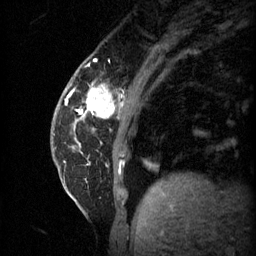
Breast MRI (dynamic contrast-enhanced), one sagittal slice. Position 13 of 60 along the scan axis. 3 images stored at this slice position (order not interpretable as contrast timing). 1.5 T. TE 4.2 ms, TR 11 ms. 2 mm slice thickness. 256 × 256 image matrix. Female patient, age 62 years.
Structures marked on this image (semi-automatically segmented with operator editing):
- analysis volume of interest (the breast-tissue region the enhancement analysis was run in; not a lesion): bounding box (x1, y1, x2, y2) in pixels: (55, 72, 124, 131)
- tumour enhancement mask (voxels above the 70 % enhancement threshold inside the analysis volume of interest): (67, 84, 116, 117)